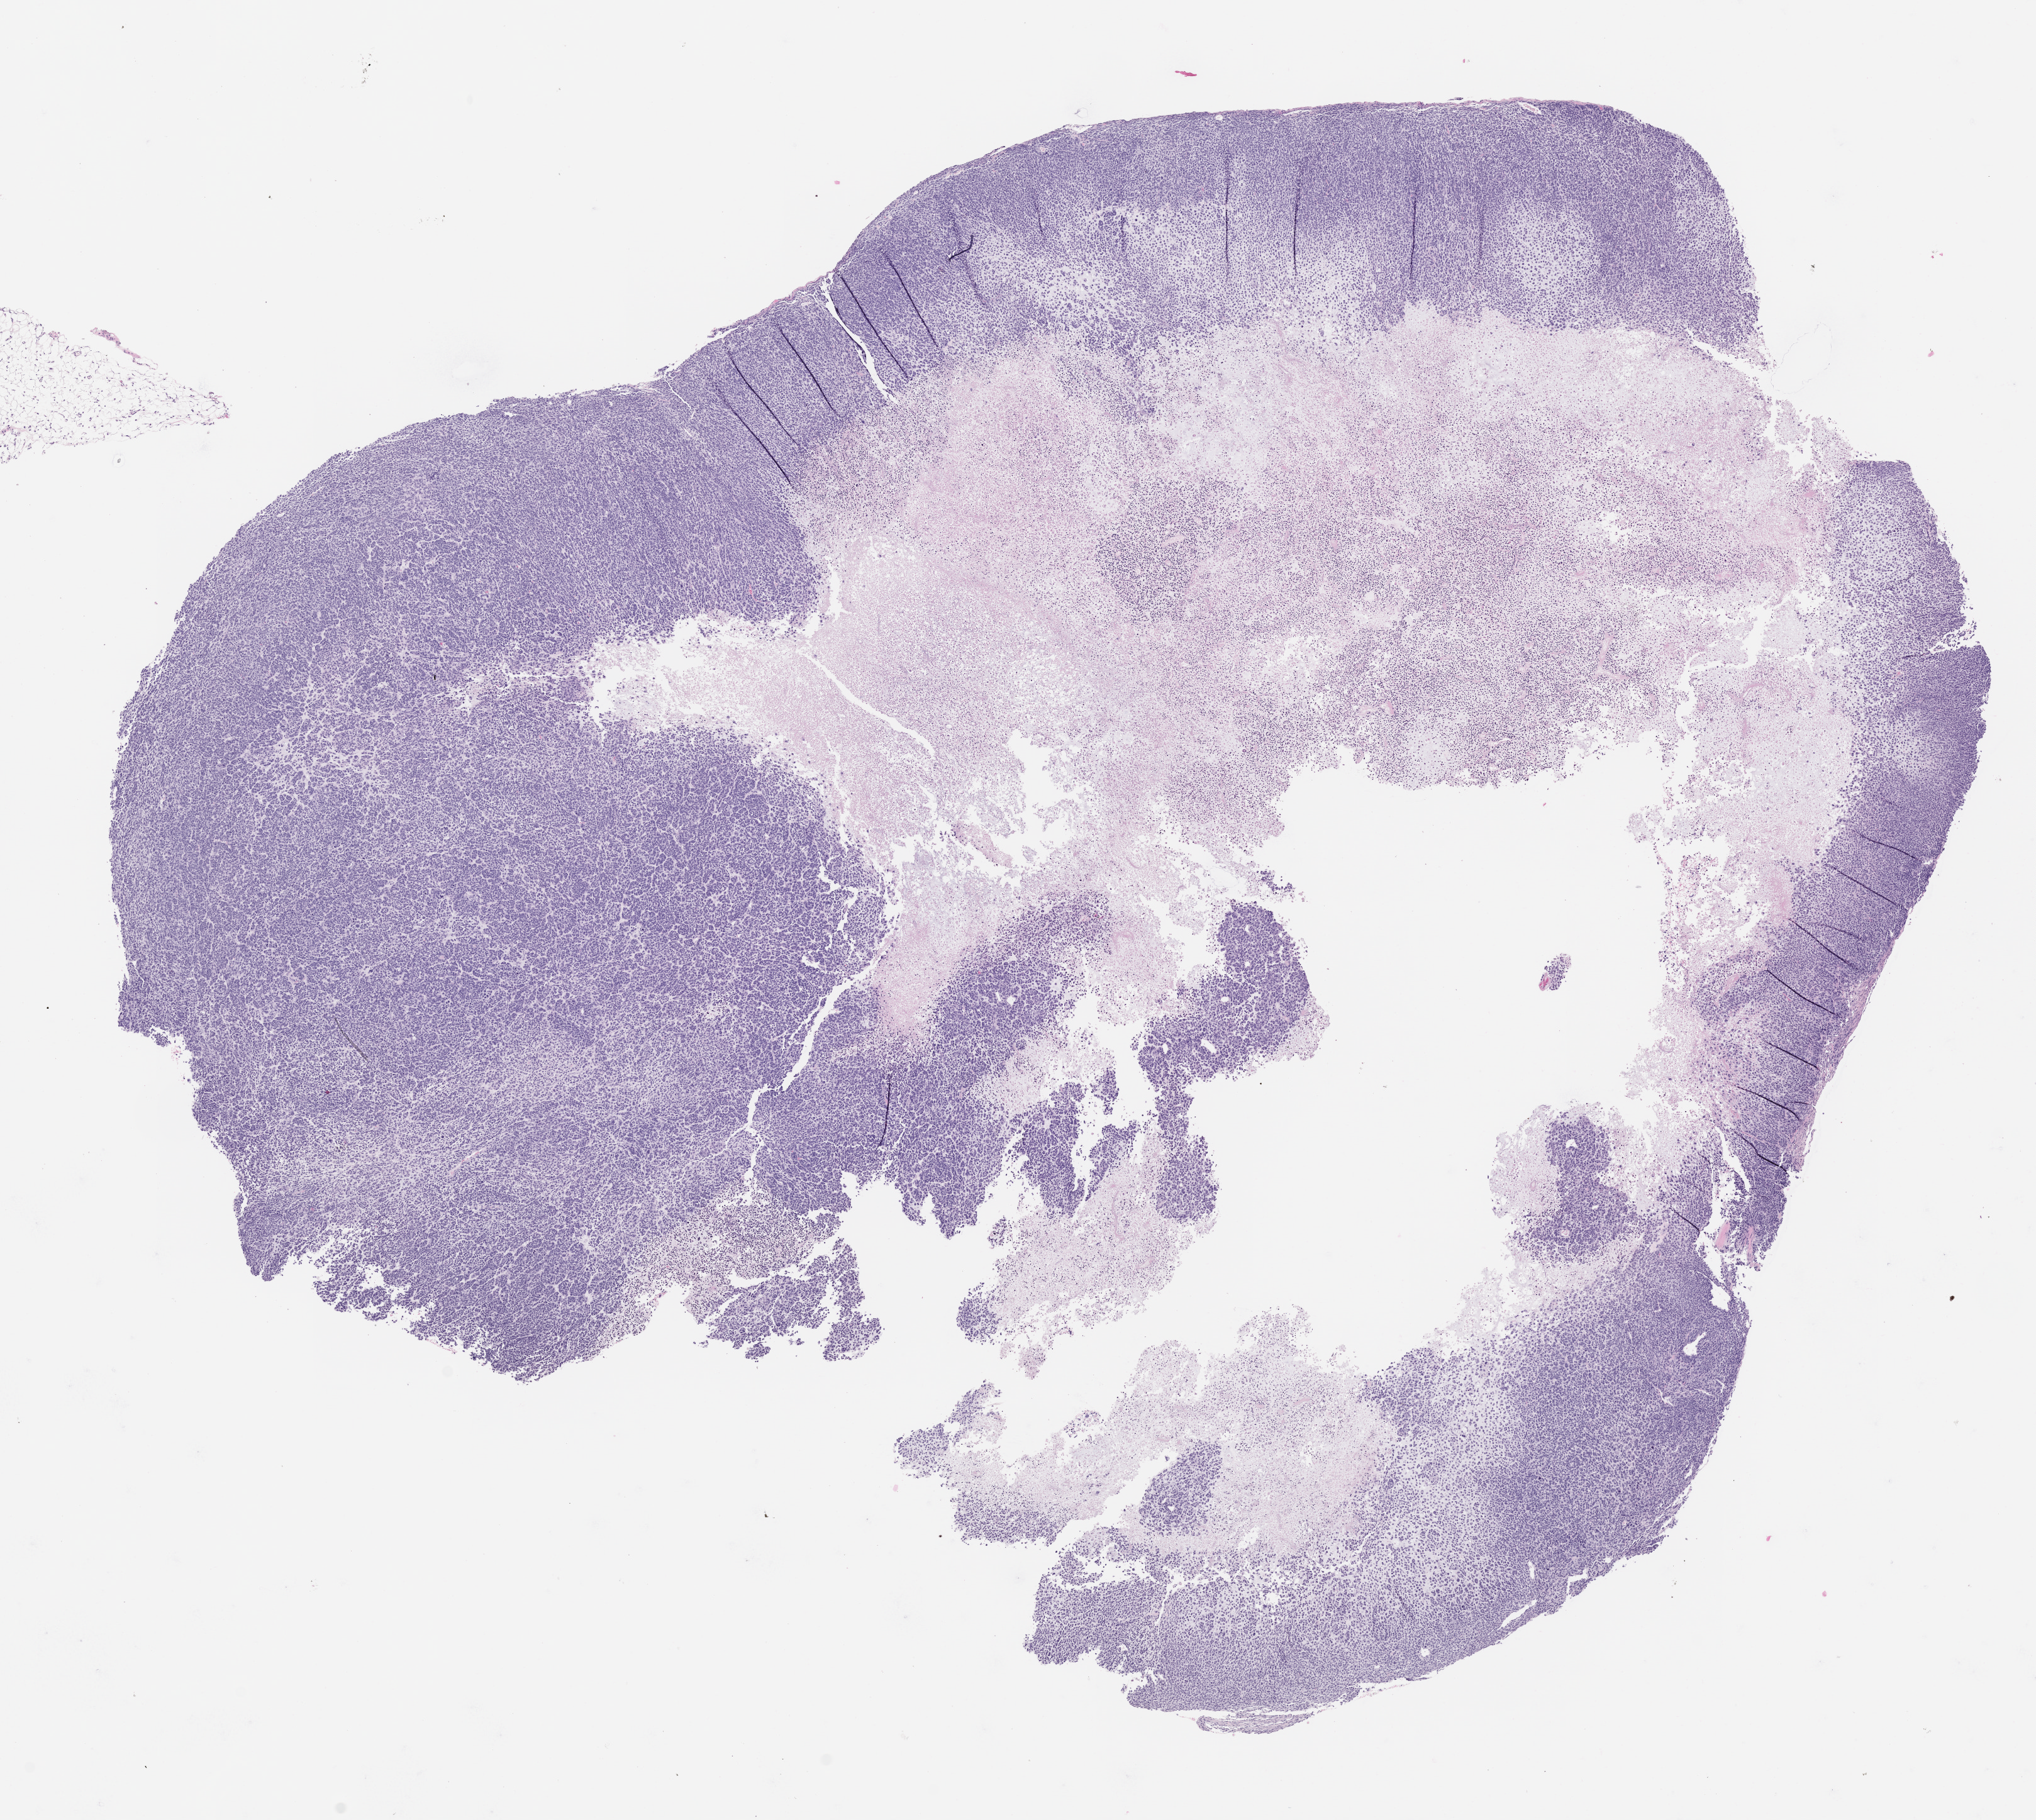
Haematoxylin and eosin whole-slide image of a patient-derived xenograft (PDX) tumor grown in a mouse, passage 1, whole scanned area (about 13.0 x 11.6 mm) shown as a low-resolution overview. FFPE section. Originating tumor site category: bladder.
- originating patient diagnosis: Urothelial Carcinoma